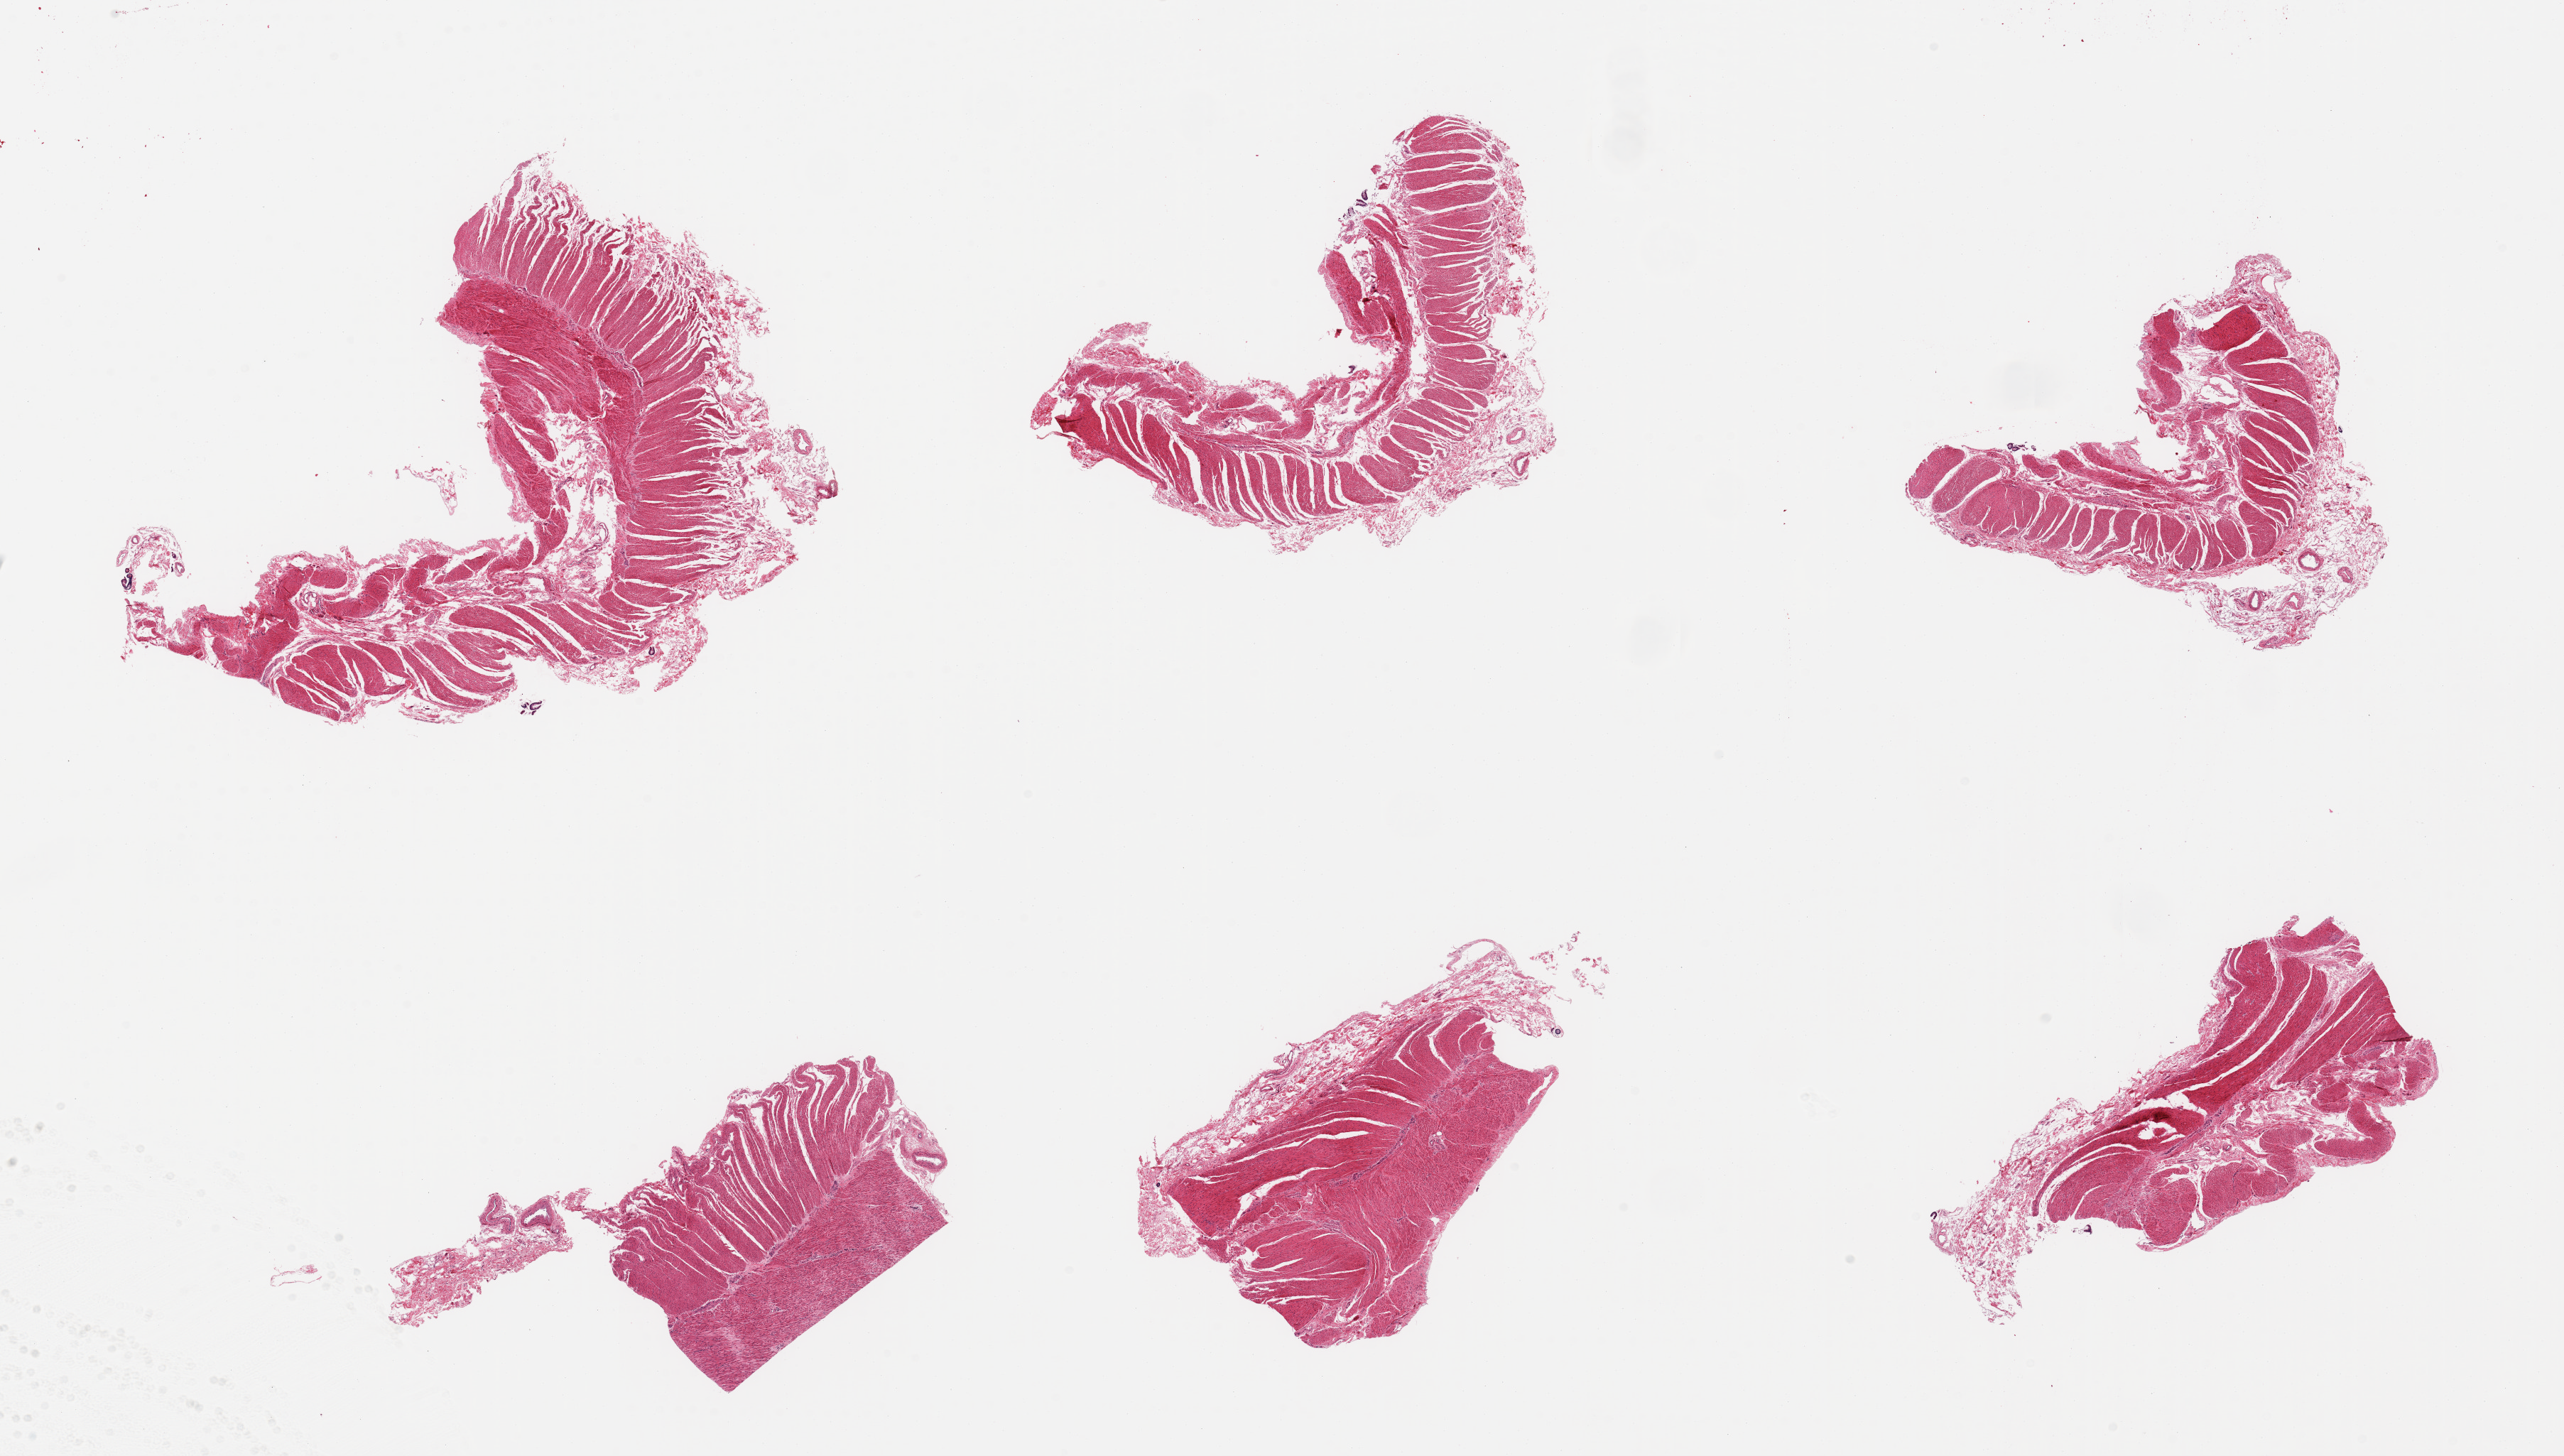
Whole-slide image, haematoxylin and eosin stain, brightfield, low-resolution overview of the scanned area, about 28.5 x 16.2 mm (slide scanned at 20x). PAXgene-fixed, paraffin-embedded tissue. Target tissue: transverse colon. Tissue donor sample. Donor: male.
• reviewer comment on this tissue sample: 6 pieces; muscularis withup to 0.8mm attached fat/vessels